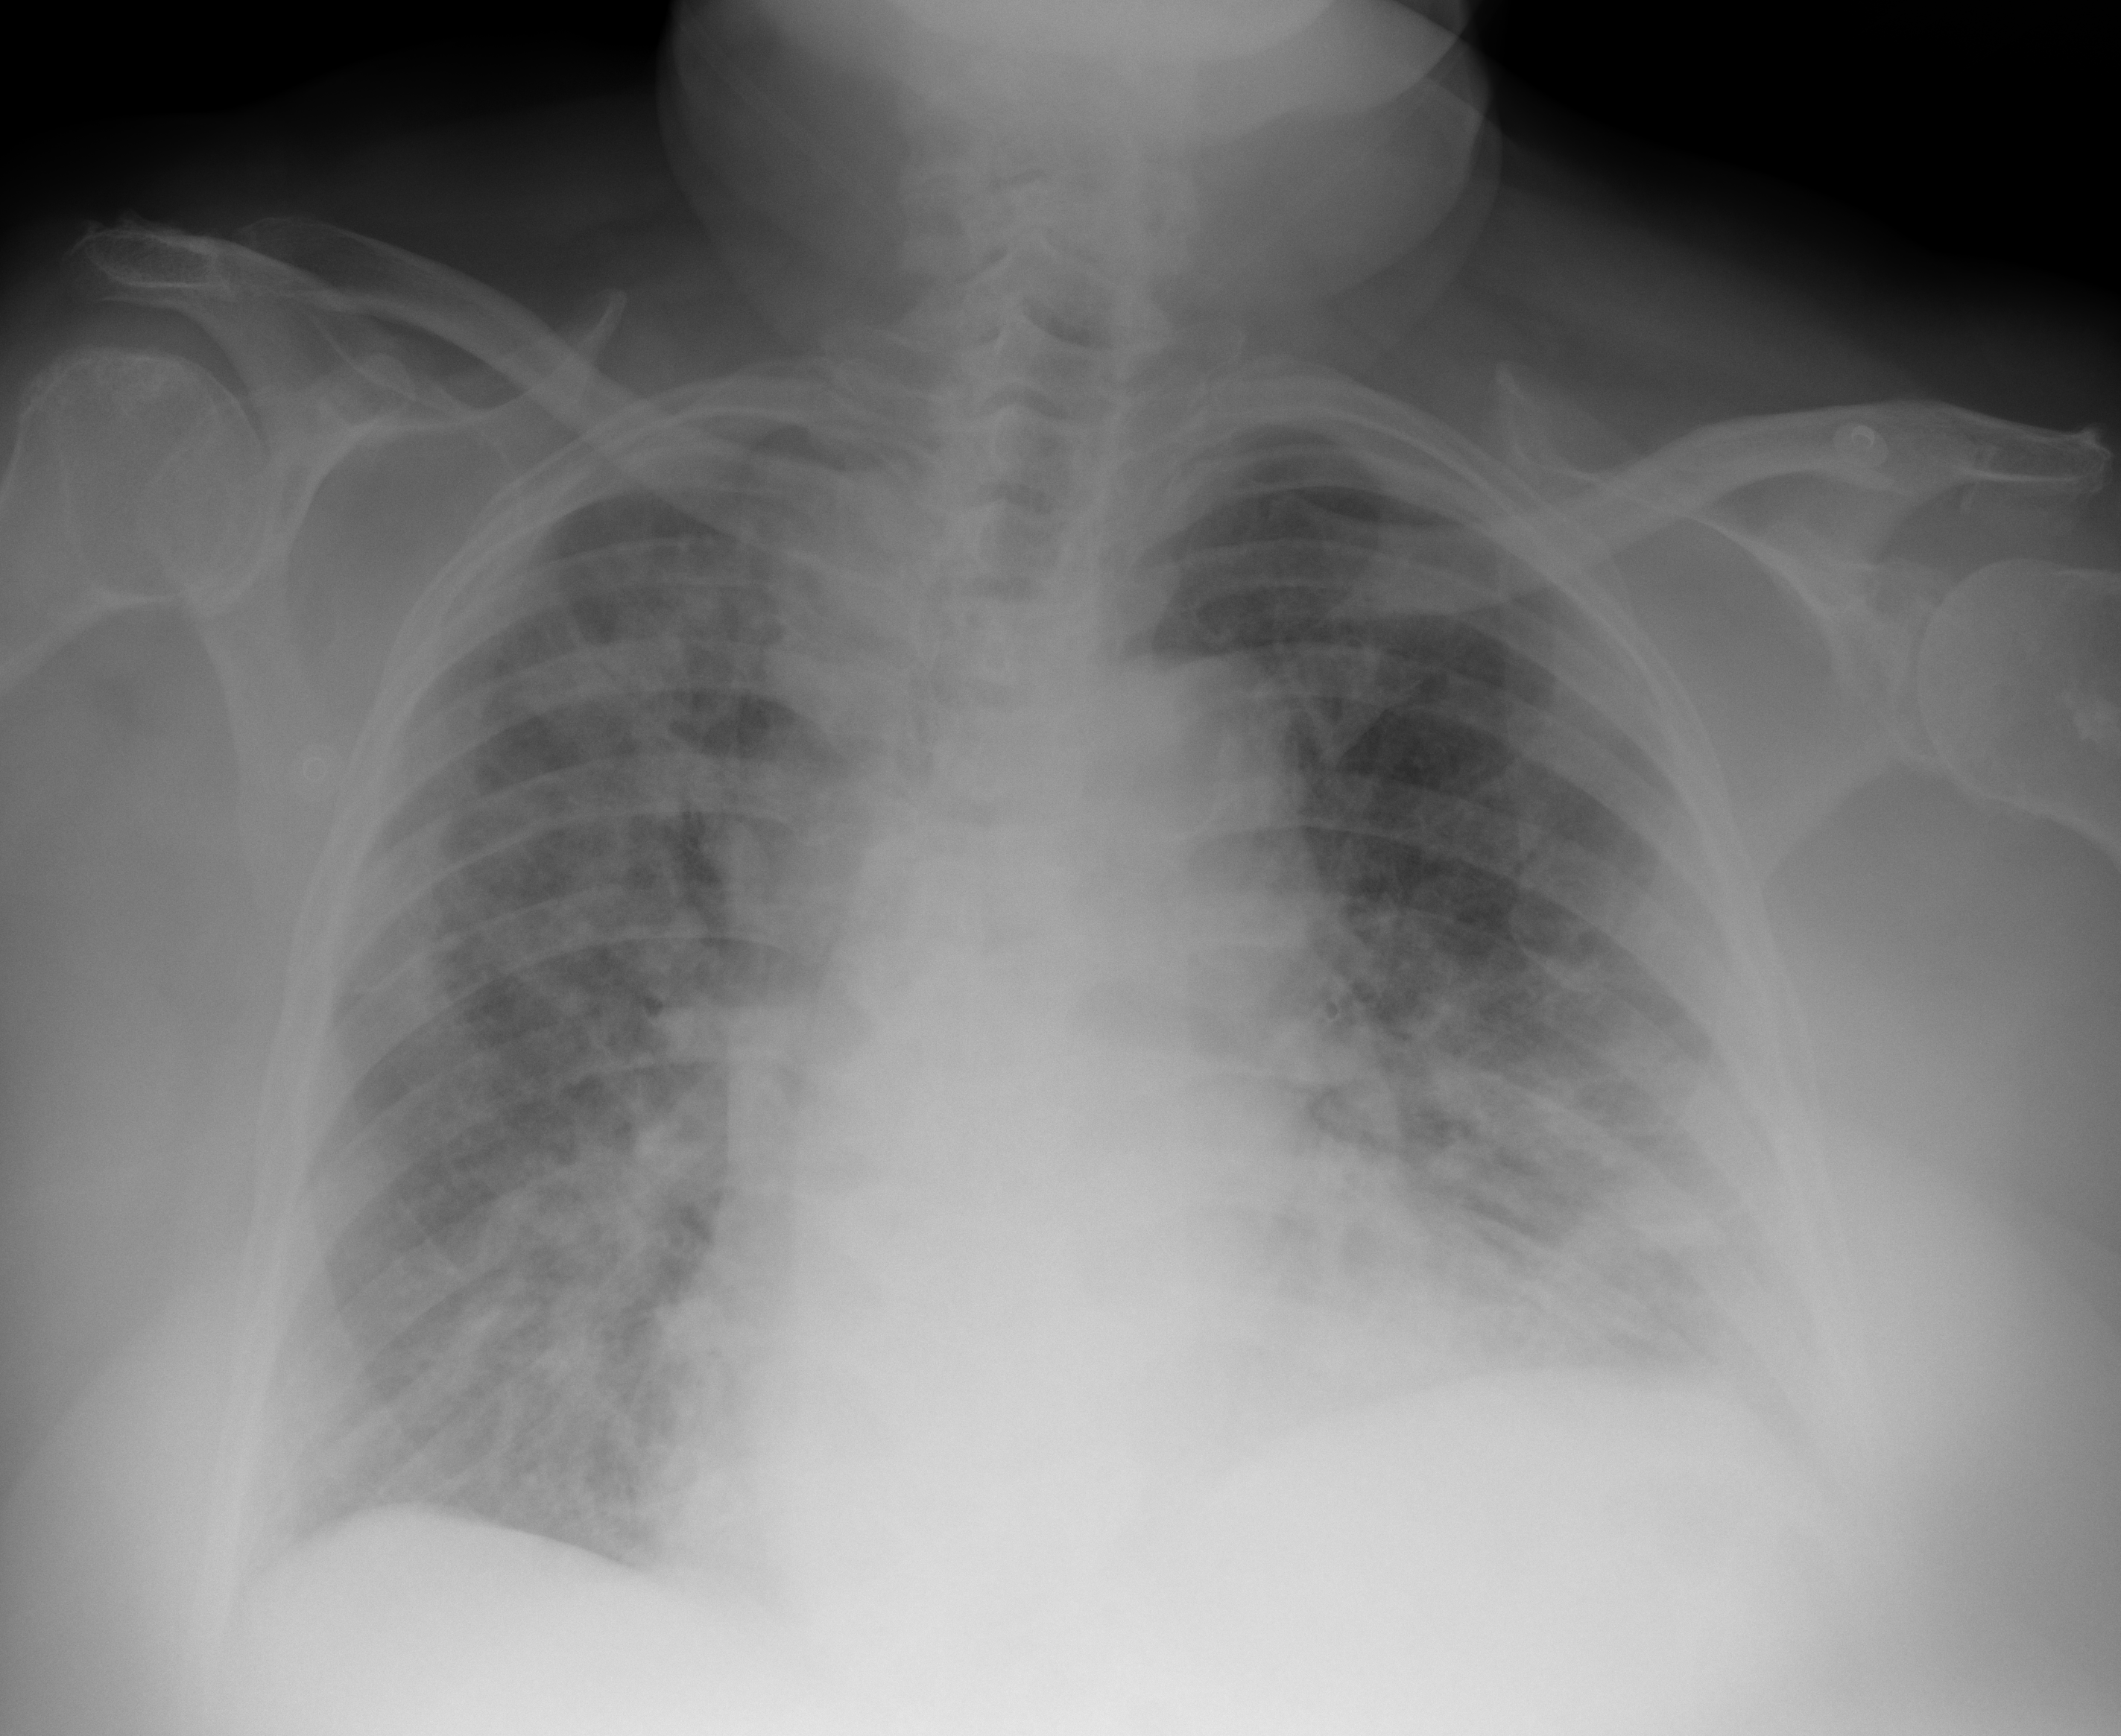
Chest X-ray (portable), AP projection. Female patient, age 73 years; imaged 0 days after the COVID-19 diagnosis.
Radiologist's key findings for this exam: multiple patchy ill-defined airspace opacities bilaterally.